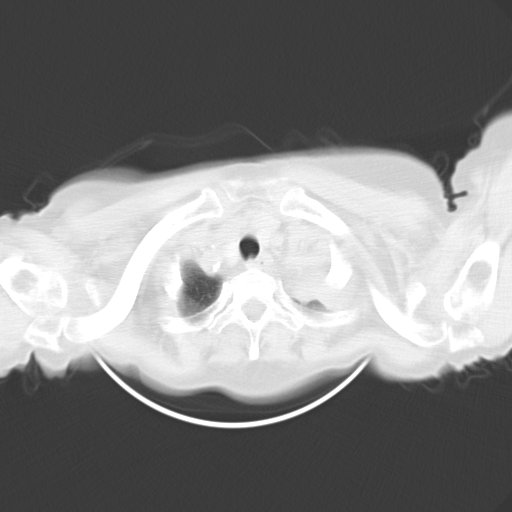
Chest CT, one axial slice; slice 25 of 26 in the series (ordered by position); reconstruction kernel B40f; 120 kVp; lung window (W 1500 / L -600 HU); 10 mm slice thickness; 512 × 512 image matrix, field of view 353 × 353 mm. Patient: female, 71 years. From the clinical record (not read from this slice): clinical TNM (as recorded): T3 N3 M0.
Structures marked on this image (bounding box drawn by a radiologist):
- lung tumour (recorded histology: adenocarcinoma): bounding box (x1, y1, x2, y2) in pixels: (285, 239, 360, 323)